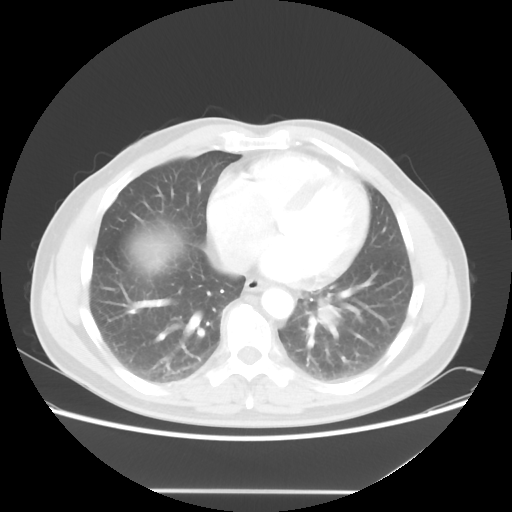
Chest CT, one axial slice. Slice 22 of 56 in the series (ordered by position). 120 kVp. Lung window (W 1500 / L -600 HU). 5 mm slice thickness. 512 × 512 image matrix. Male patient, age 61 years. Case-level facts recorded for this patient, not image findings: clinical TNM (as recorded): T1c N0 M0; histopathological grade: G3.
Annotated regions visible in this slice (bounding box drawn by a radiologist):
- lung tumour (recorded histology: adenocarcinoma): bounding box <310,297,352,340> (left, top, right, bottom; pixels)